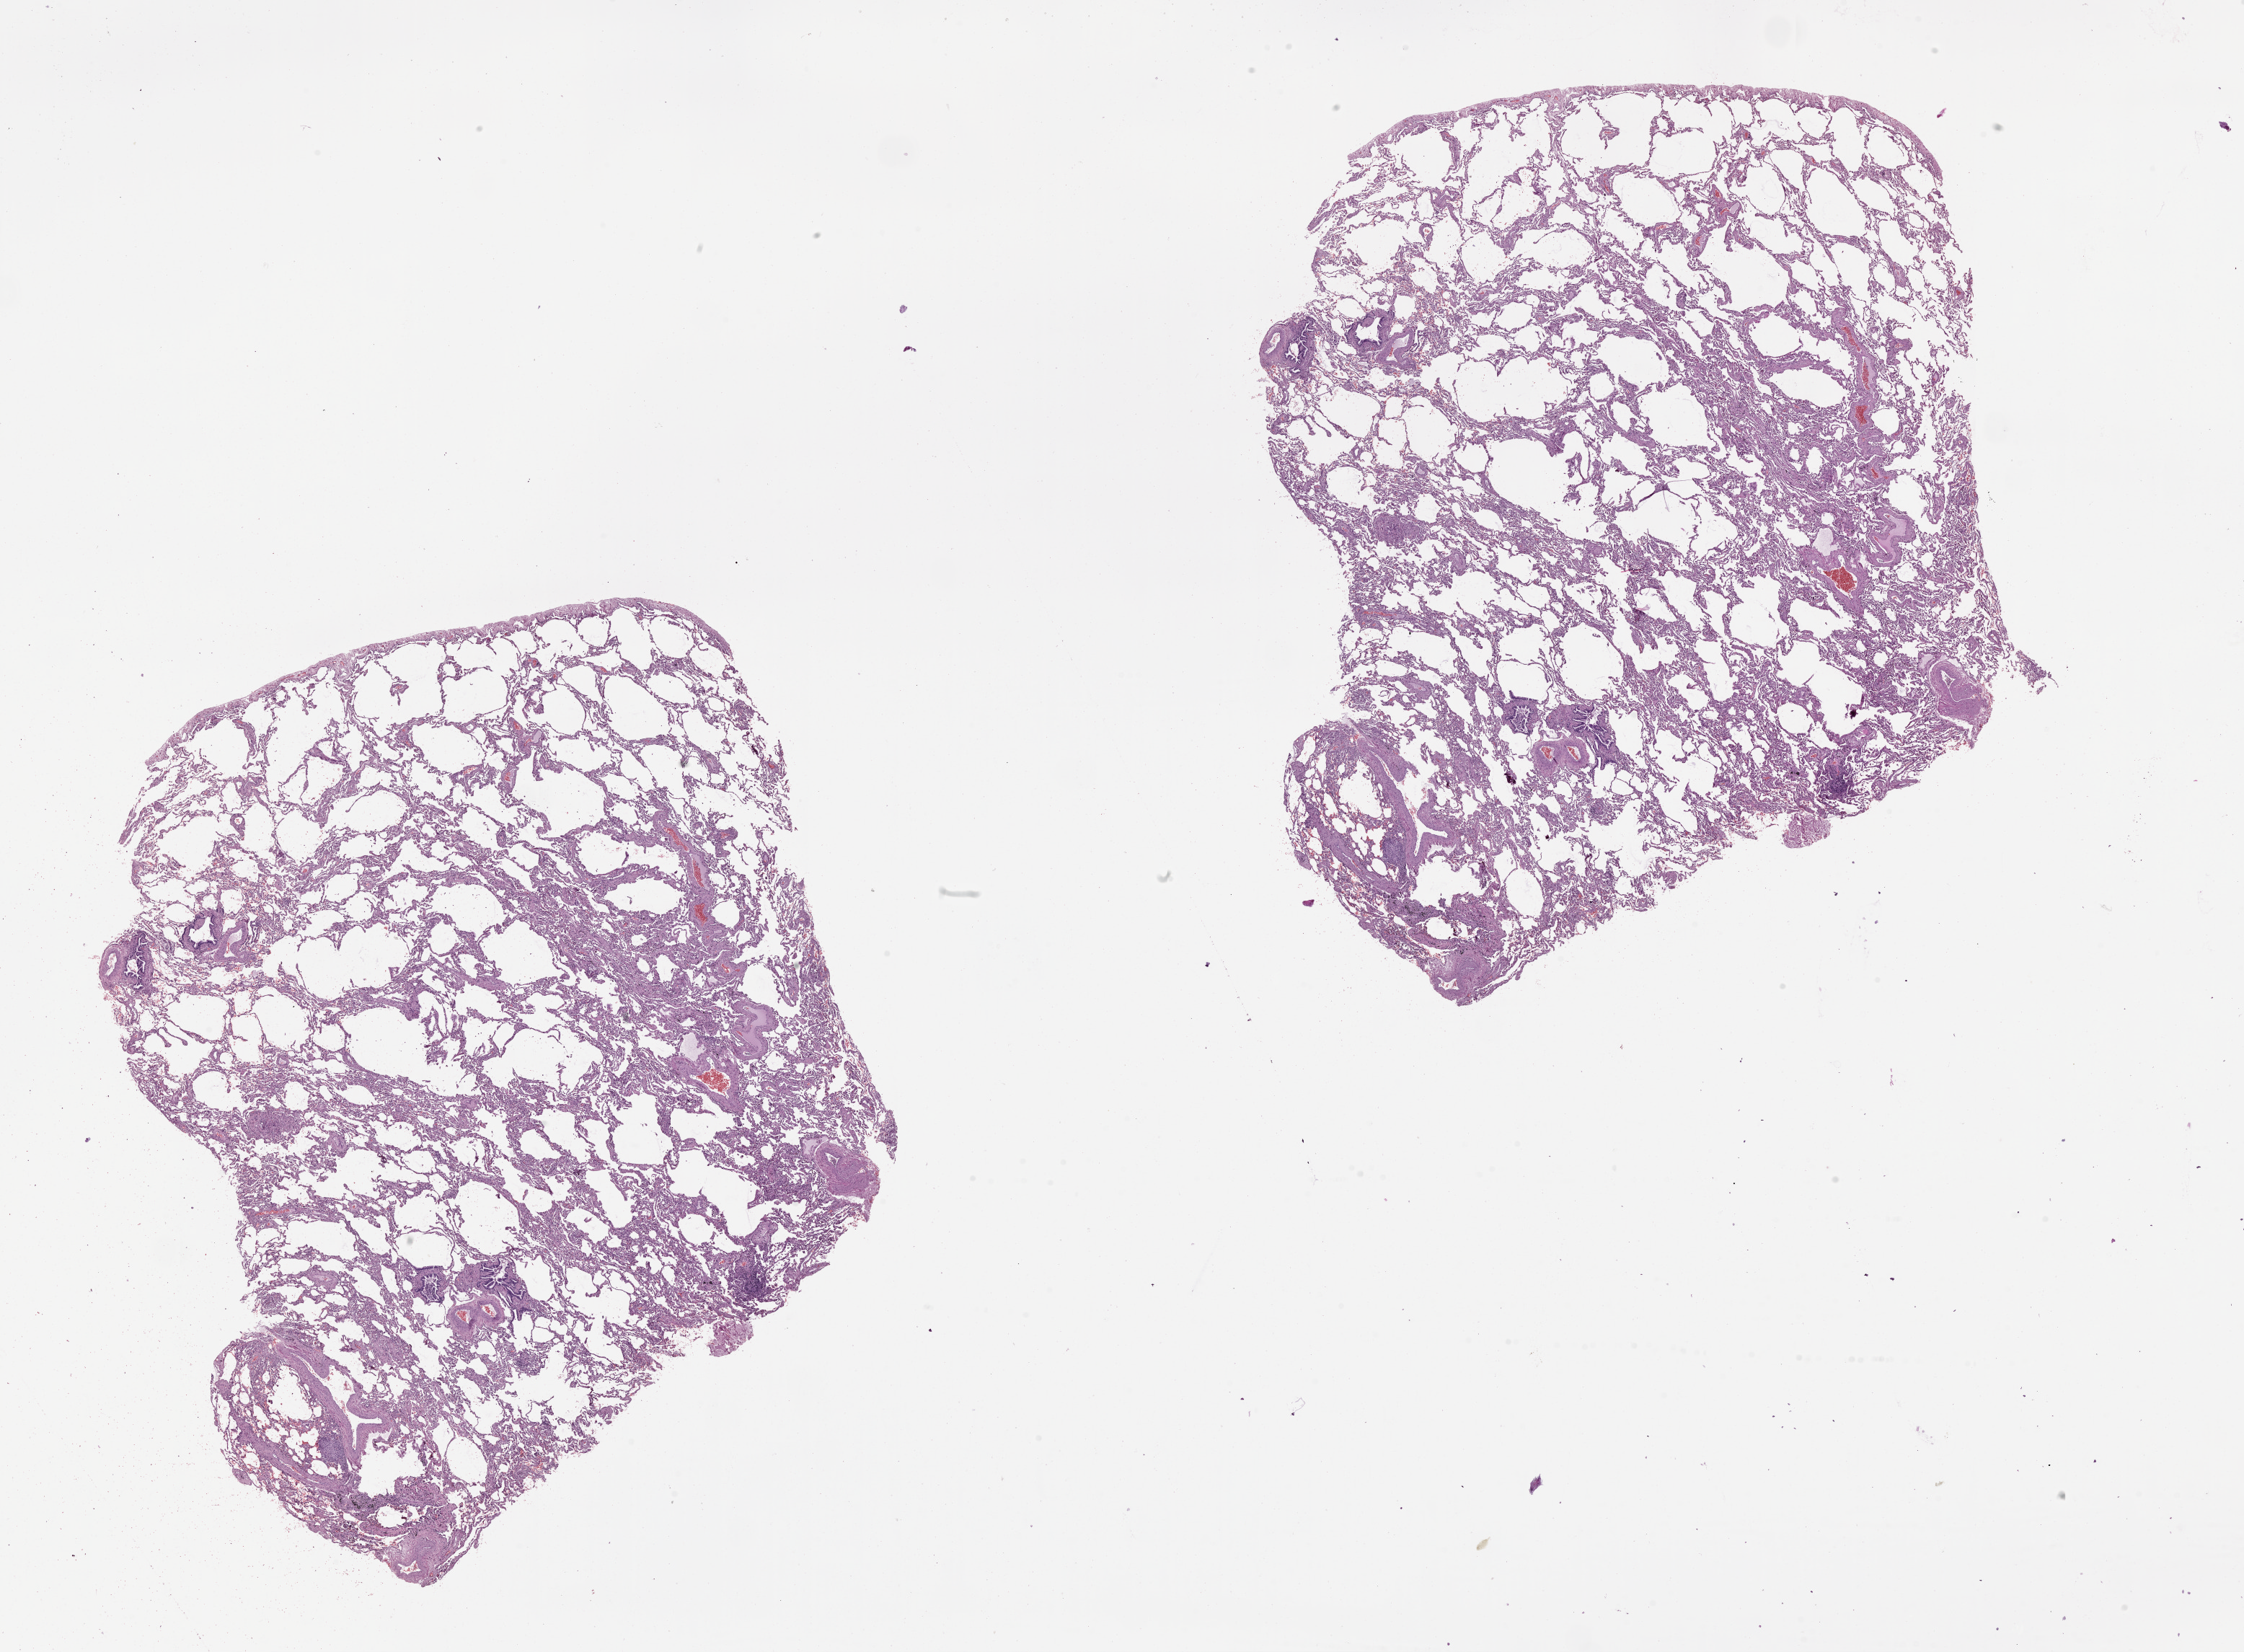
Whole-slide histology image, H&E-stained, whole scanned area (about 25.1 x 18.4 mm) shown as a low-resolution overview. Lung, normal (non-tumour) tissue. Patient: male, age 67 years.
This section: normal (non-tumour) tissue from the same patient. Patient diagnosis (cohort enrolment): squamous cell carcinoma (lung).